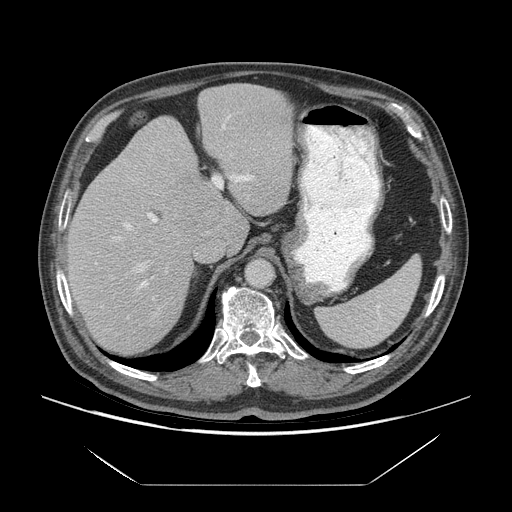
Contrast-enhanced abdominal CT (liver protocol), one axial slice. Slice 47 of 75 in the series (ordered by position). Reconstruction kernel STANDARD. 140 kVp. Soft-tissue window (W 400 / L 40 HU). 2.5 mm slice thickness. 512 × 512 image matrix. Case-level facts recorded for this patient, not image findings: diagnosis: hepatocellular carcinoma (patient treated with transarterial chemoembolisation; whether this scan precedes or follows treatment is not stated here); TNM stage (as recorded): Stage-I; Child-Pugh class: A; tumour nodularity: uninodular; tumour size: 5.8 cm.
Annotated regions visible in this slice (semi-automatic segmentation, software-assisted and operator-edited):
- liver parenchyma outside the tumour (the mass and vessels are separate outlines, so this box may not span the whole liver): box from (x=66, y=84) to (x=292, y=354) px
- mass: (x=167, y=179)–(x=223, y=233)
- liver vessels: (x=95, y=115)–(x=254, y=289)